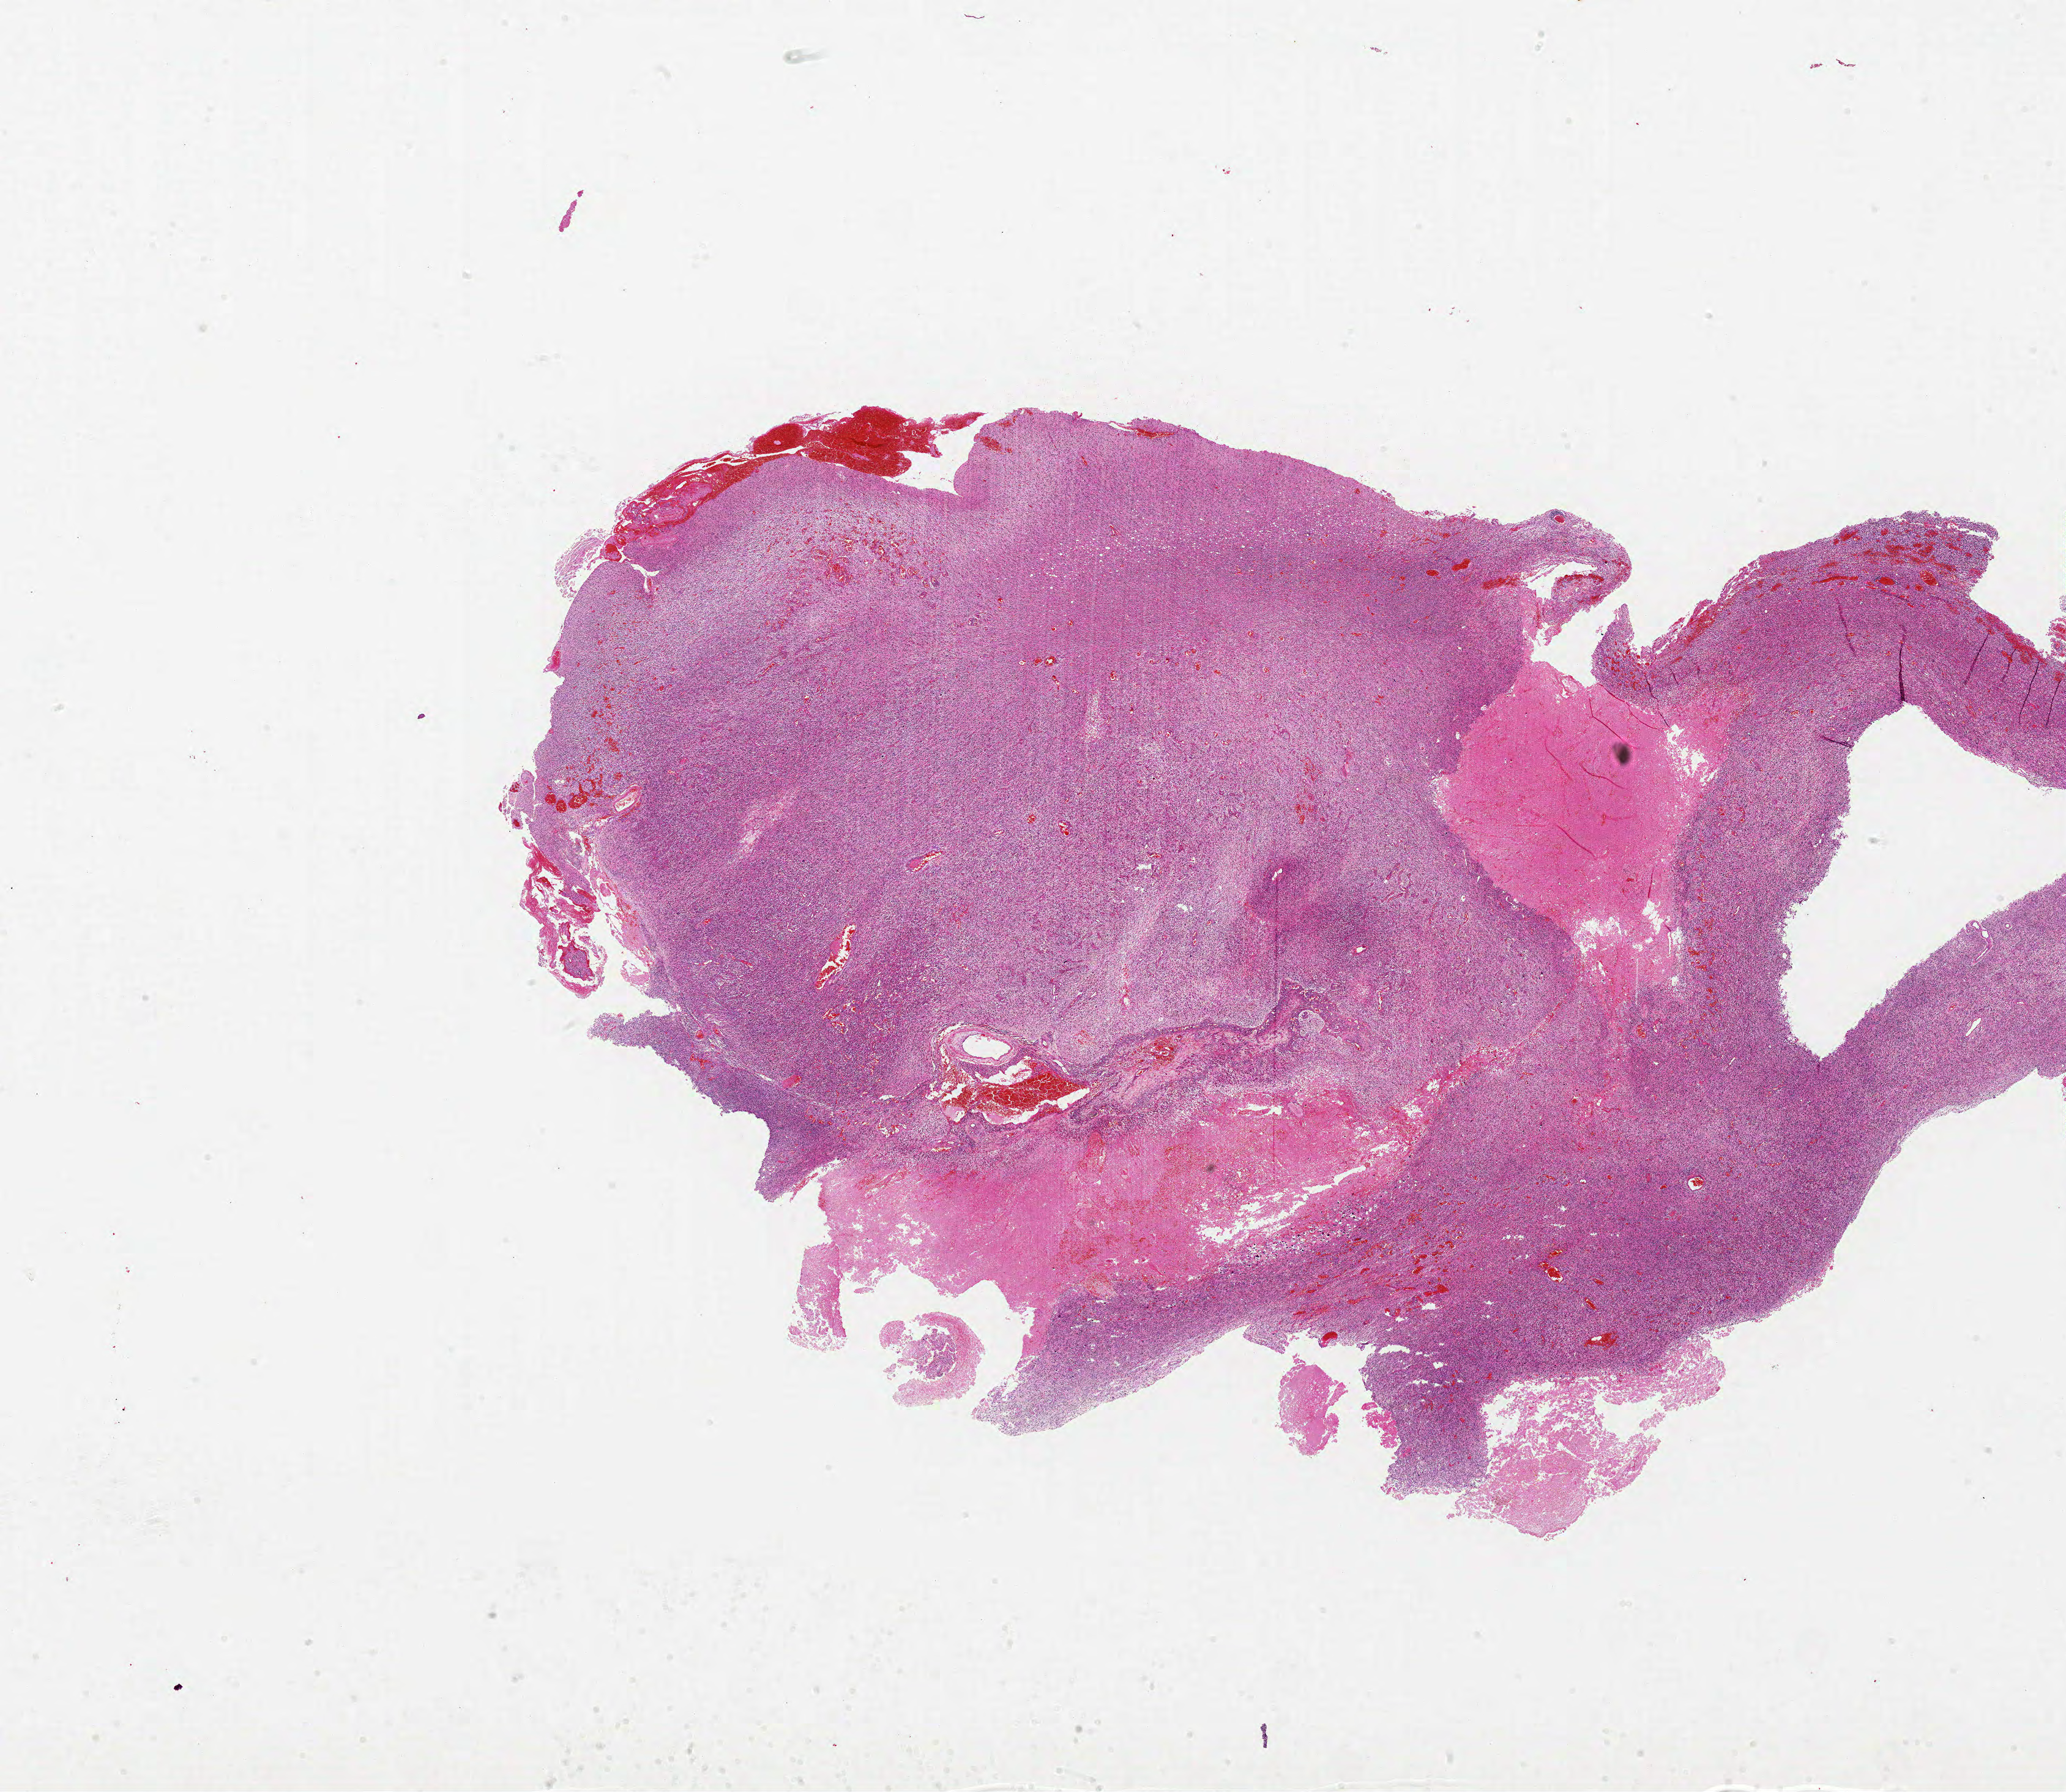
Whole-slide histology image, Hematoxylin and eosin (H&E) stained, shown as a low-resolution overview of the whole scanned area (about 27.0 x 23.4 mm), FFPE section, brain, primary tumour sample. Male, age 60 years at initial diagnosis.
Diagnosis: Glioblastoma.